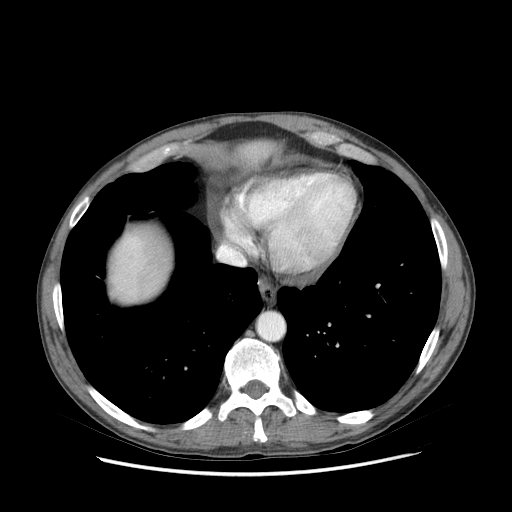
Contrast-enhanced abdominal CT (liver protocol), one axial slice; position 75 of 89 along the scan axis; reconstruction kernel STANDARD; 140 kVp; soft-tissue window (W 400 / L 40 HU); 2.5 mm slice thickness; 512 × 512 image matrix. From the clinical record (not read from this slice): diagnosis: hepatocellular carcinoma (patient treated with transarterial chemoembolisation; whether this scan precedes or follows treatment is not stated here); TNM stage (as recorded): Stage-IIIB; Child-Pugh class: A; tumour differentiation: moderately differentiated; tumour nodularity: multinodular.
Outlined on this slice (semi-automatically segmented with operator editing):
- liver parenchyma outside the tumour (the mass and vessels are separate outlines, so this box may not span the whole liver): box from (x=110, y=140) to (x=270, y=302) px
- liver vessels: (x=124, y=238)–(x=140, y=269)